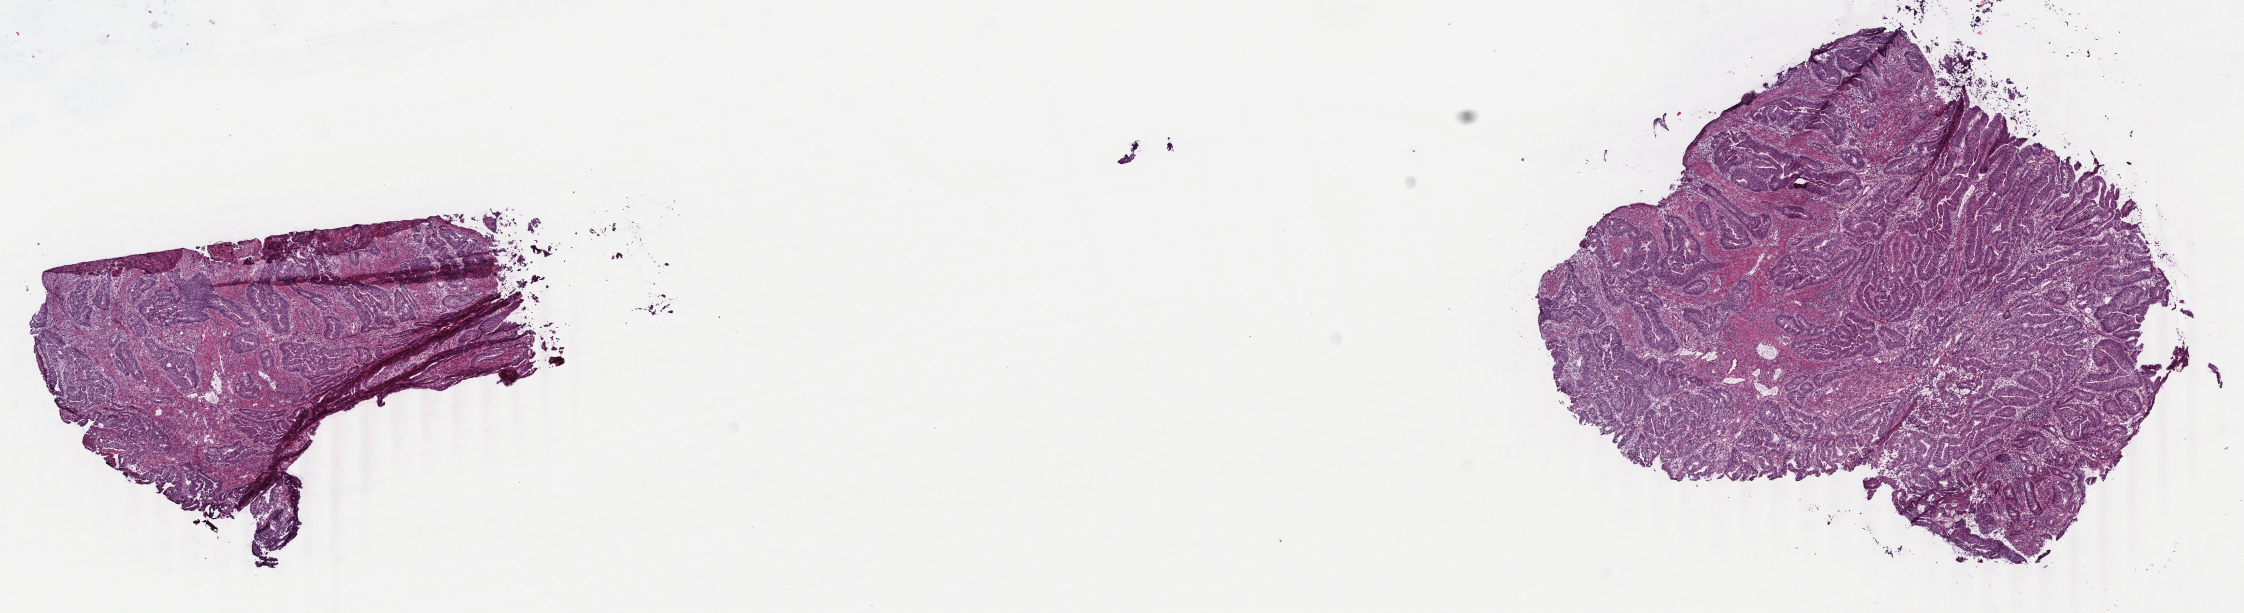
Hematoxylin and eosin (H&E) stained whole-slide image, a low-resolution overview of the entire scanned area, about 17.8 x 4.9 mm (acquisition: 40x scan). Frozen section from the top of the tissue portion. Primary tumour sample from the rectum. Male, age 58 years at initial diagnosis. Composition of this section per pathologist review: tumour cells 85%, tumour nuclei 75%, normal cells 0%, stromal cells 14%, necrosis 1%. Infiltration values recorded for this section: lymphocyte infiltration 15%, monocyte infiltration 3%, neutrophil infiltration 2%.
TNM: T3 N1 M0. AJCC pathologic stage: IIIB (6th edition). Pathologic diagnosis: Adenocarcinoma, NOS. Lymph nodes positive (case pathology): 2 of 47 examined.